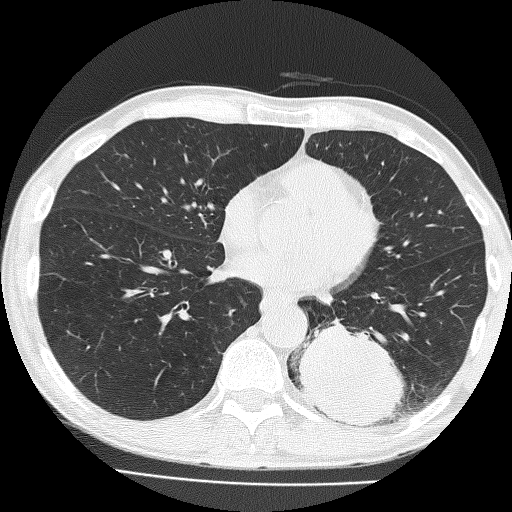
Chest CT (low-dose screening protocol), one axial image, baseline screening round, lung window (W 1500 / L -600 HU), 2 mm slice thickness, 120 kVp, 512 × 512 image matrix, field of view 324 × 324 mm. Male participant, aged 58 years at enrolment. Current smoker at enrolment.
Lesion marked by an expert reader, bounding box (x1, y1, x2, y2) in pixels: (298, 307, 422, 434). The screening reader recorded 2 non-calcified nodules or masses ≥4 mm on this exam (left lower lobe, left upper lobe); which of them this box marks is not recorded. Official screen result: positive, change unspecified: nodule(s) >= 4 mm or enlarging nodule(s), mass(es), or other non-specific abnormalities suspicious for lung cancer. Participant outcome: lung cancer diagnosed 39 days after this screen — non-small cell carcinoma, left lower lobe, poorly differentiated (G3), stage IV (AJCC 6th edition), 74 mm at pathology.